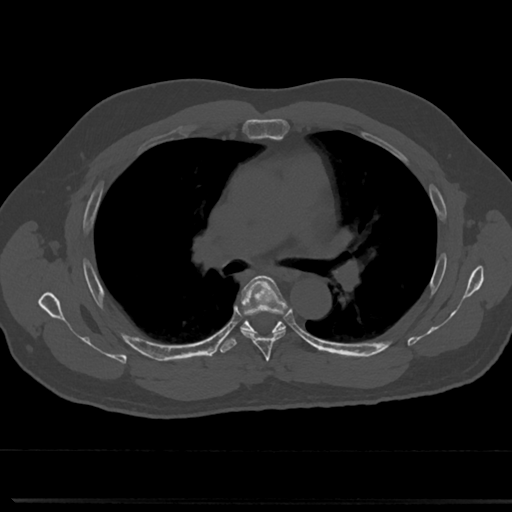
CT including the spine, one axial slice; slice 482 of 817 in the series (ordered by position); 120 kVp; bone window (W 1800 / L 400 HU); 512 × 512 image matrix. Male patient, age 61 years. From the clinical record (not read from this slice): primary cancer: prostate.
Structures marked on this image (semi-automatically segmented with operator editing):
- T4 vertebra: bounding box [x1, y1, x2, y2] px = [267, 368, 271, 373]
- T5 vertebra: [238, 278, 288, 355]
- T6 vertebra: [242, 326, 286, 333]